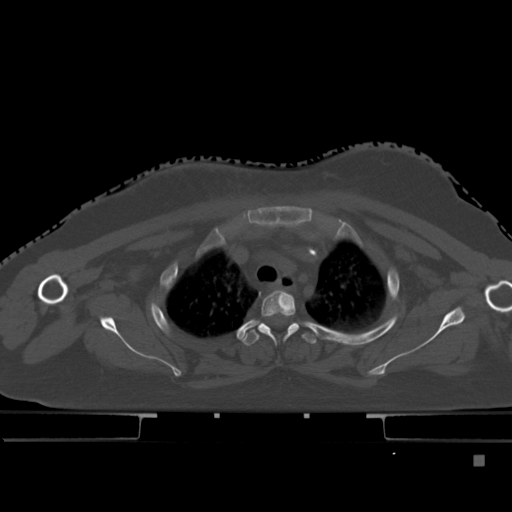
CT including the spine, one axial slice; bone window (W 1800 / L 400 HU); 1.5 mm slice thickness; 512 × 512 image matrix, field of view 404 × 404 mm. Patient: female, 33 years. From the clinical record (not read from this slice): primary cancer: breast.
Structures marked on this image (semi-automatic segmentation, software-assisted and operator-edited):
- T2 vertebra: bounding box (x1, y1, x2, y2) in pixels: (259, 290, 299, 339)
- T3 vertebra: (241, 322, 317, 345)